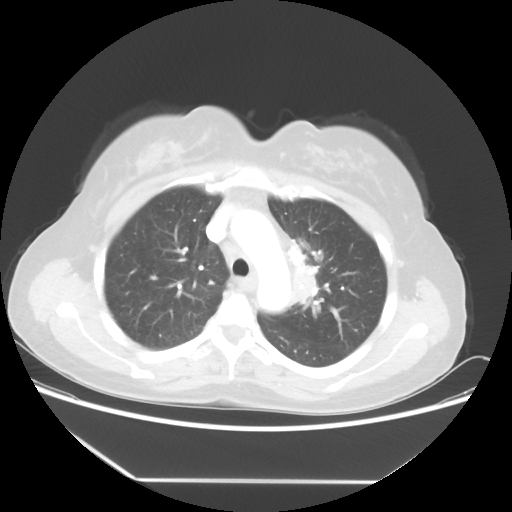
Chest CT, one axial slice. Slice 38 of 52 in the series (ordered by position). Reconstruction kernel STANDARD. Lung window (W 1500 / L -600 HU). 5 mm slice thickness. 512 × 512 image matrix, field of view 390 × 390 mm. Patient: female, 50 years. Case-level facts recorded for this patient, not image findings: clinical TNM (as recorded): T2 N3 M0.
Annotated regions visible in this slice (bounding box drawn by a radiologist):
- lung tumour (recorded histology: adenocarcinoma): bounding box [x1, y1, x2, y2] px = [287, 256, 328, 315]